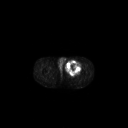
FDG PET of an extremity soft-tissue mass (from a PET/CT study), one axial slice. Position 252 of 267 along the scan axis. 3.27 mm slice thickness. 128 × 128 image matrix, field of view 700 × 700 mm. Patient: male, 63 years. Case-level facts recorded for this patient, not image findings: histological type: pleiomorphic liposarcoma; grade: high; site of the primary tumour: left thigh.
Annotated regions visible in this slice (expert contour drawn on MRI and transferred to this co-registered scan by the dataset authors):
- gross tumour volume including surrounding oedema: bounding box [x1, y1, x2, y2] px = [65, 60, 82, 74]
- gross tumour volume (mass): [65, 60, 81, 74]